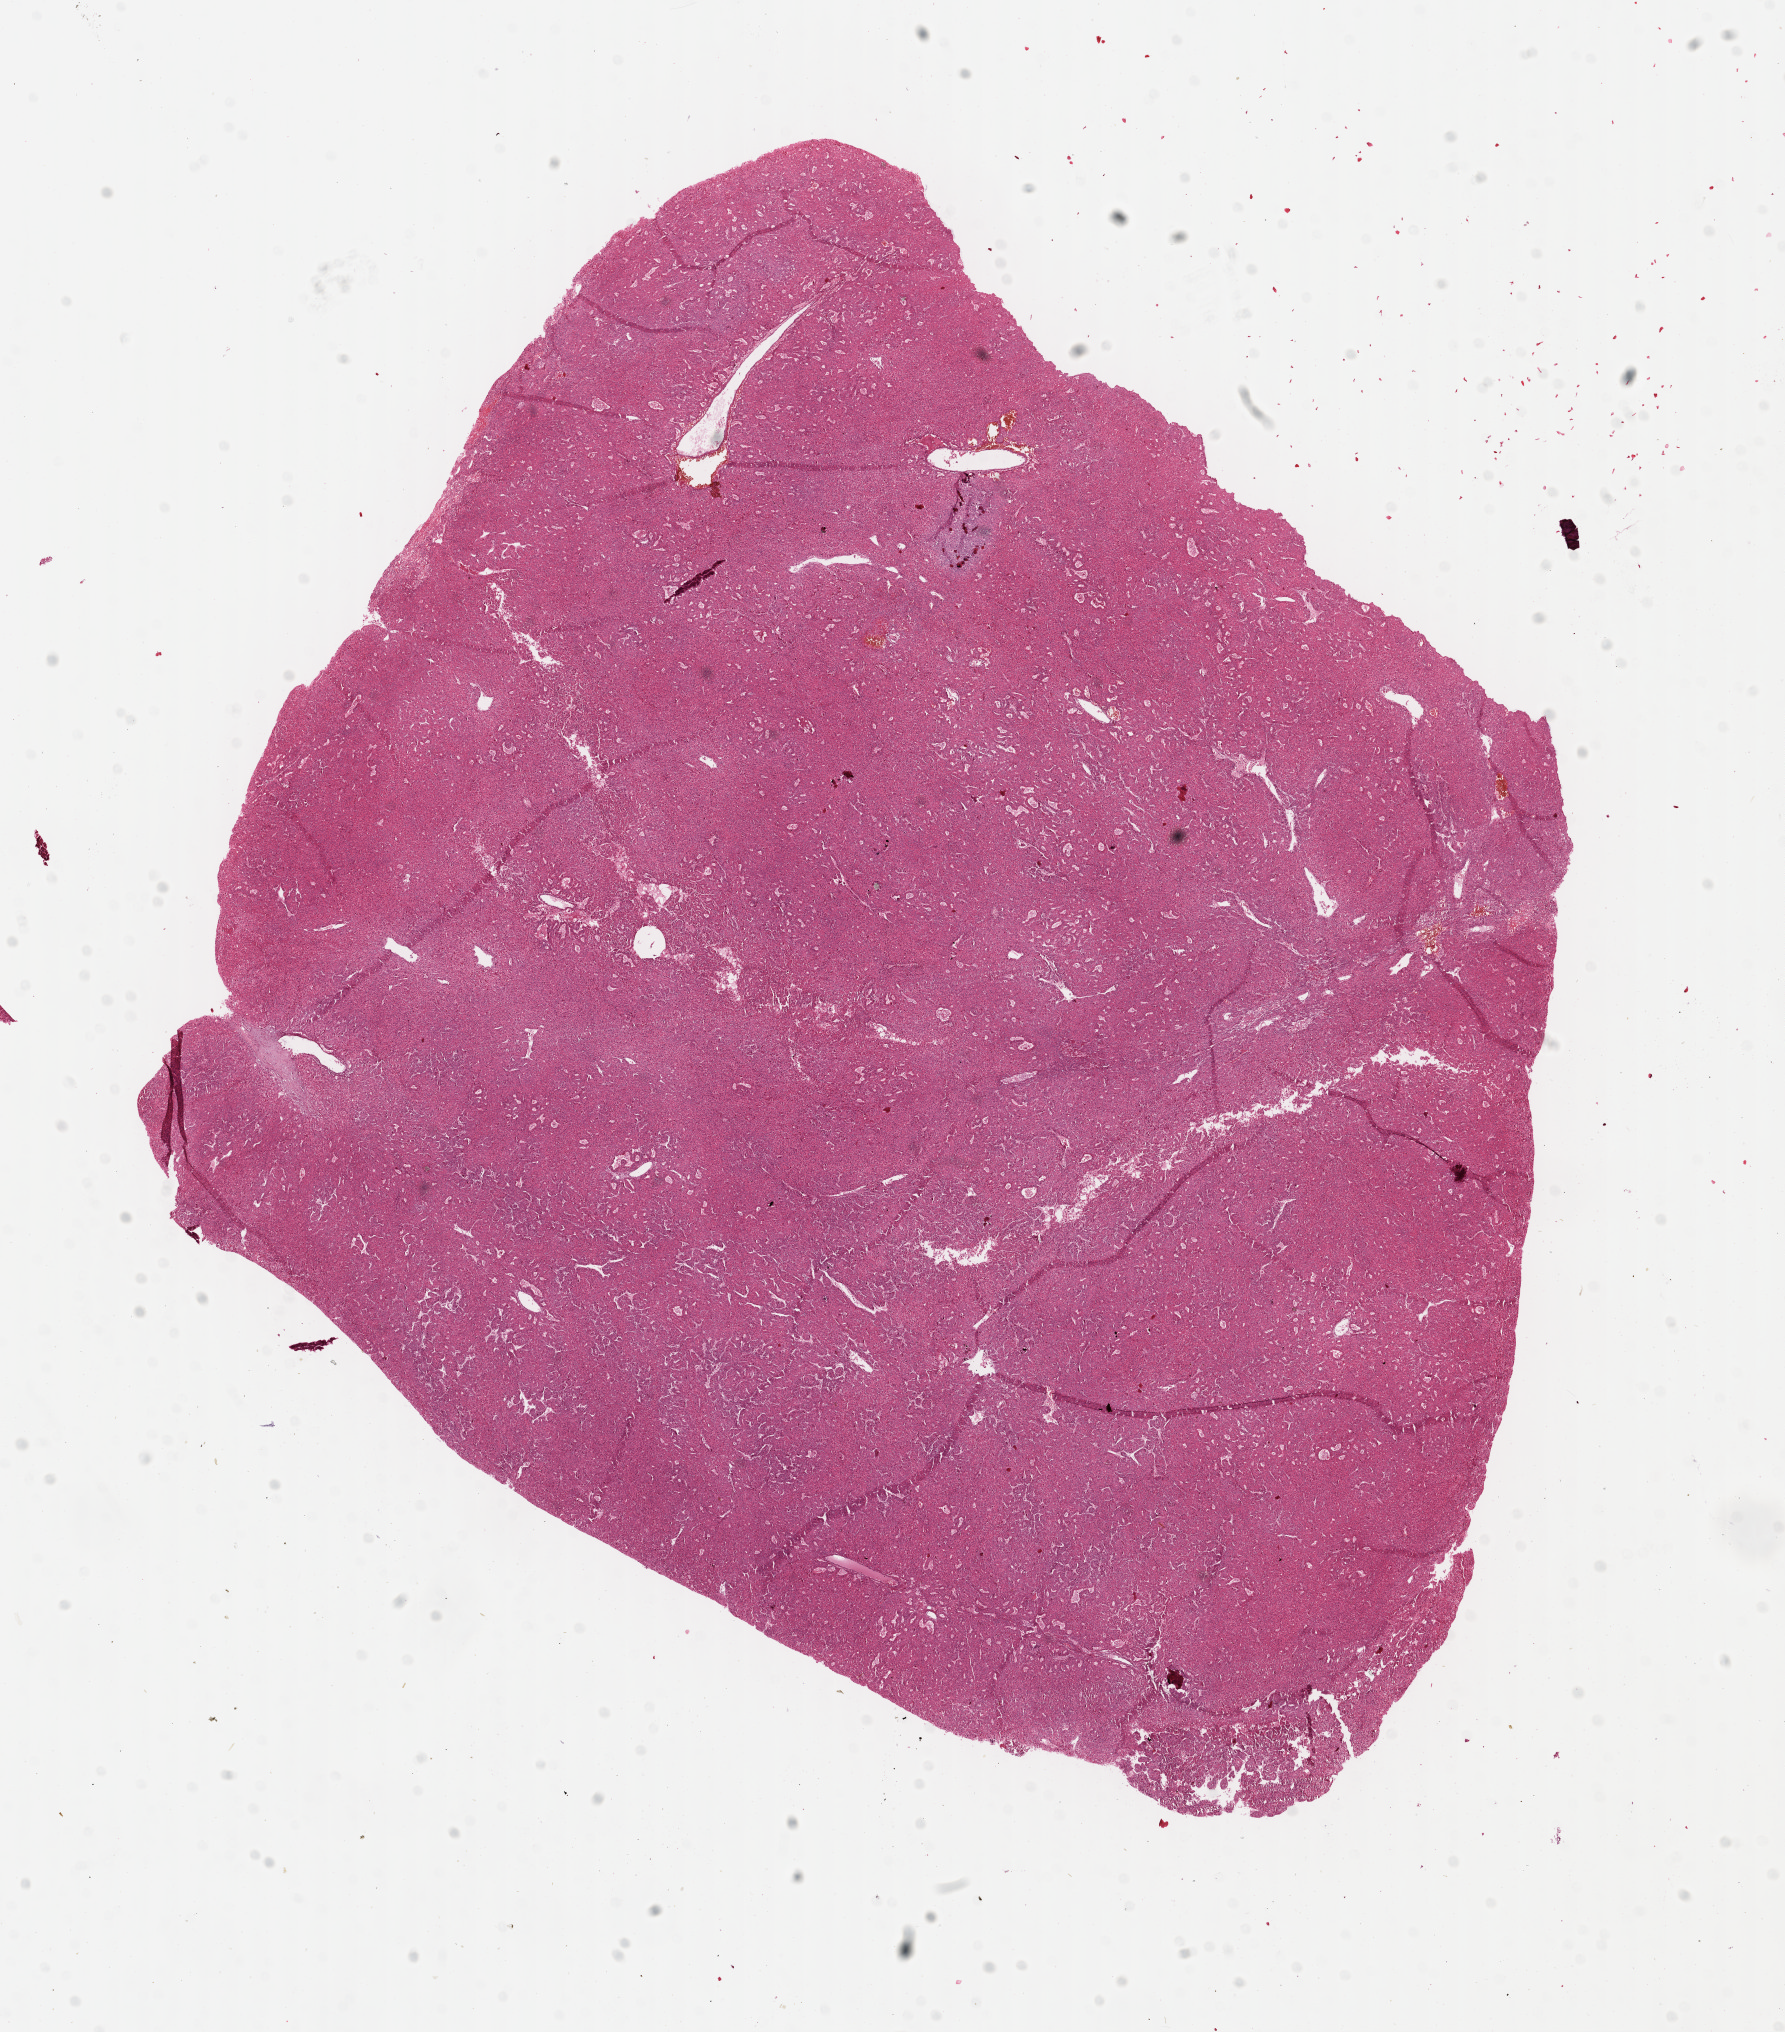
H&E-stained whole-slide image, a low-resolution overview of the entire scanned area, about 14.0 x 16.0 mm (acquisition: 40x scan); formalin-fixed paraffin-embedded (FFPE) diagnostic section; sample: primary tumour, liver. Male patient; age at initial diagnosis 67 years. Histologic grade: G1 (well differentiated).
AJCC pathologic stage: IIIC (7th edition). Histologic diagnosis: Hepatocellular carcinoma, NOS. TNM: T4 N0 M0.